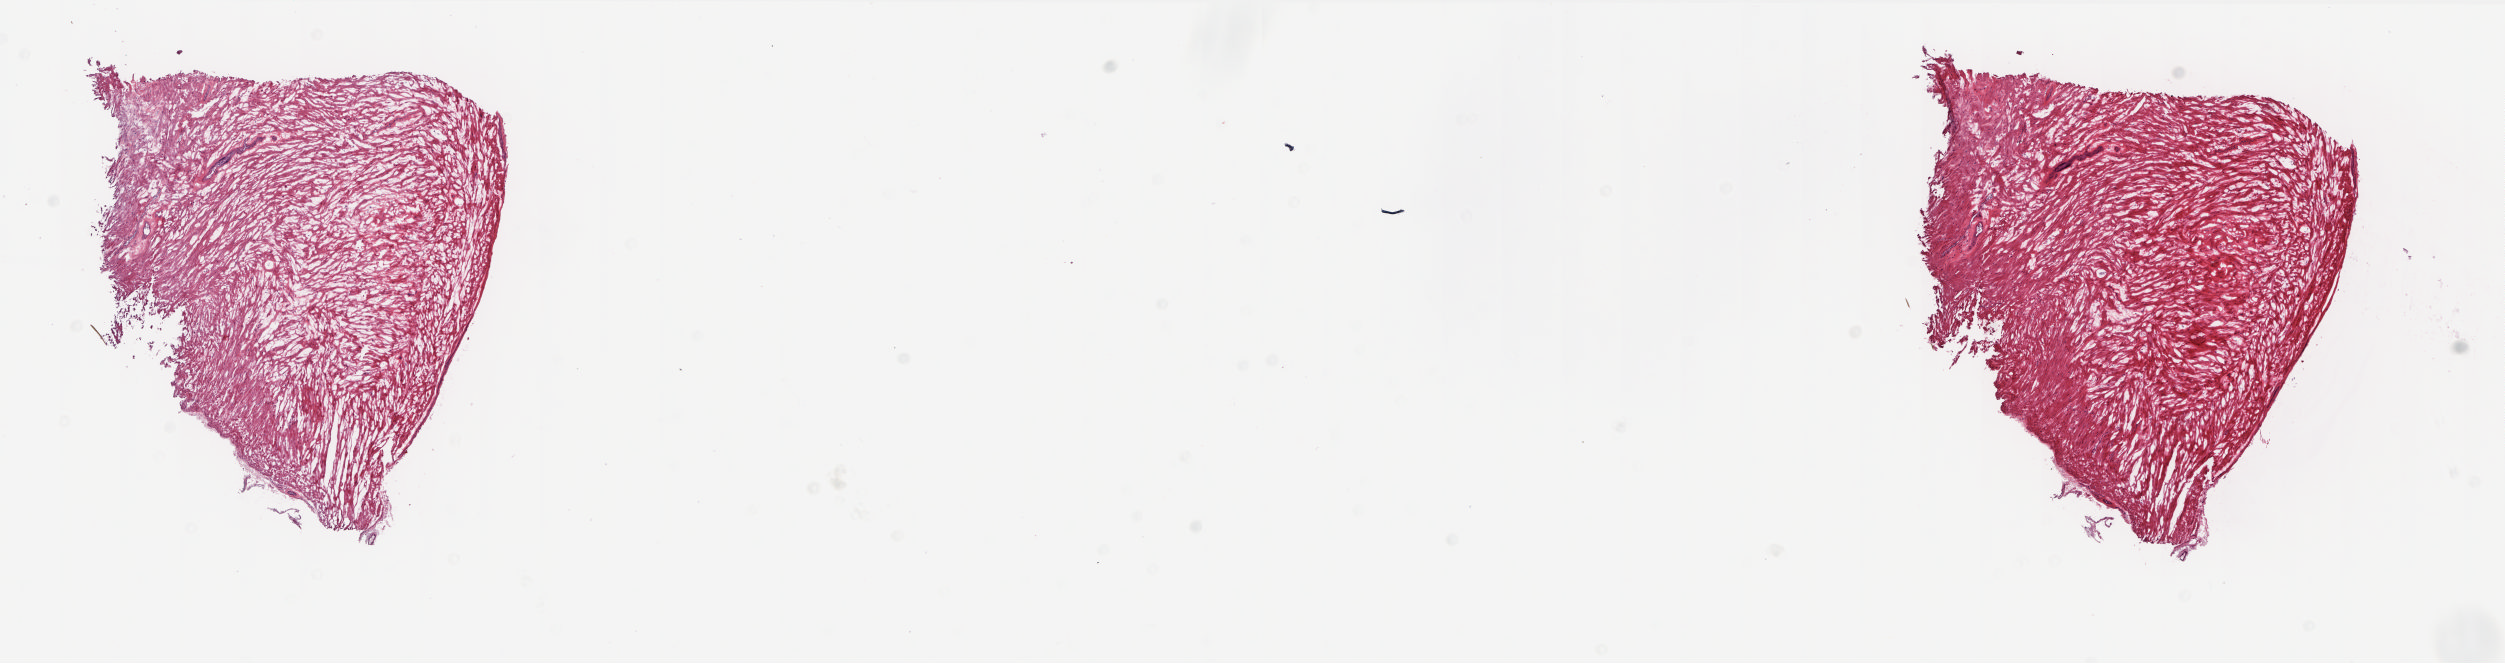
Whole-slide histology image, H&E-stained, shown as a low-resolution overview of the whole scanned area (about 20.2 x 5.3 mm, slide scanned at 20x); frozen section from the top of the tissue portion; sample: solid tissue normal (non-tumour tissue), prostate. Male patient; age at initial diagnosis 57 years. Composition of this section per pathologist review: tumour cells 0%, tumour nuclei 0%, normal cells 100%, stromal cells 0%, necrosis 0%. Infiltration values recorded for this section: lymphocyte infiltration 0%, monocyte infiltration 0%, neutrophil infiltration 0%.
This section: solid tissue normal (non-tumour) sample from the same patient. Patient diagnosis: Adenocarcinoma, NOS (prostate gland).